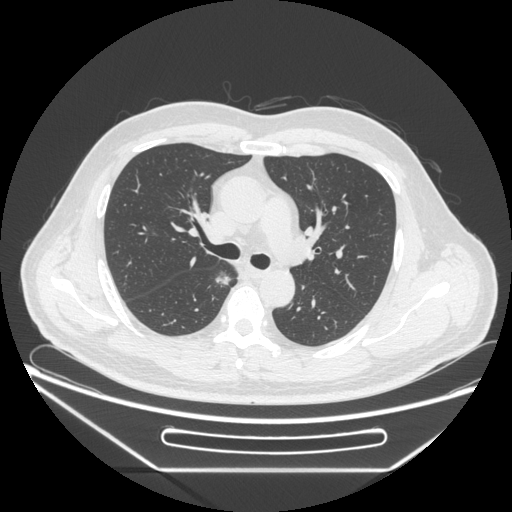
Chest CT, one axial slice. Slice 162 of 271 in the series (ordered by position). Reconstruction kernel STANDARD. Lung window (W 1500 / L -600 HU). 512 × 512 image matrix, field of view 414 × 414 mm. Patient: male, 49 years. From the clinical record (not read from this slice): clinical TNM (as recorded): T1b N0 M0; histopathological grade: G2.
Annotated regions visible in this slice (bounding box drawn by a radiologist):
- lung tumour (recorded histology: adenocarcinoma): bounding box [x1, y1, x2, y2] px = [208, 265, 234, 289]